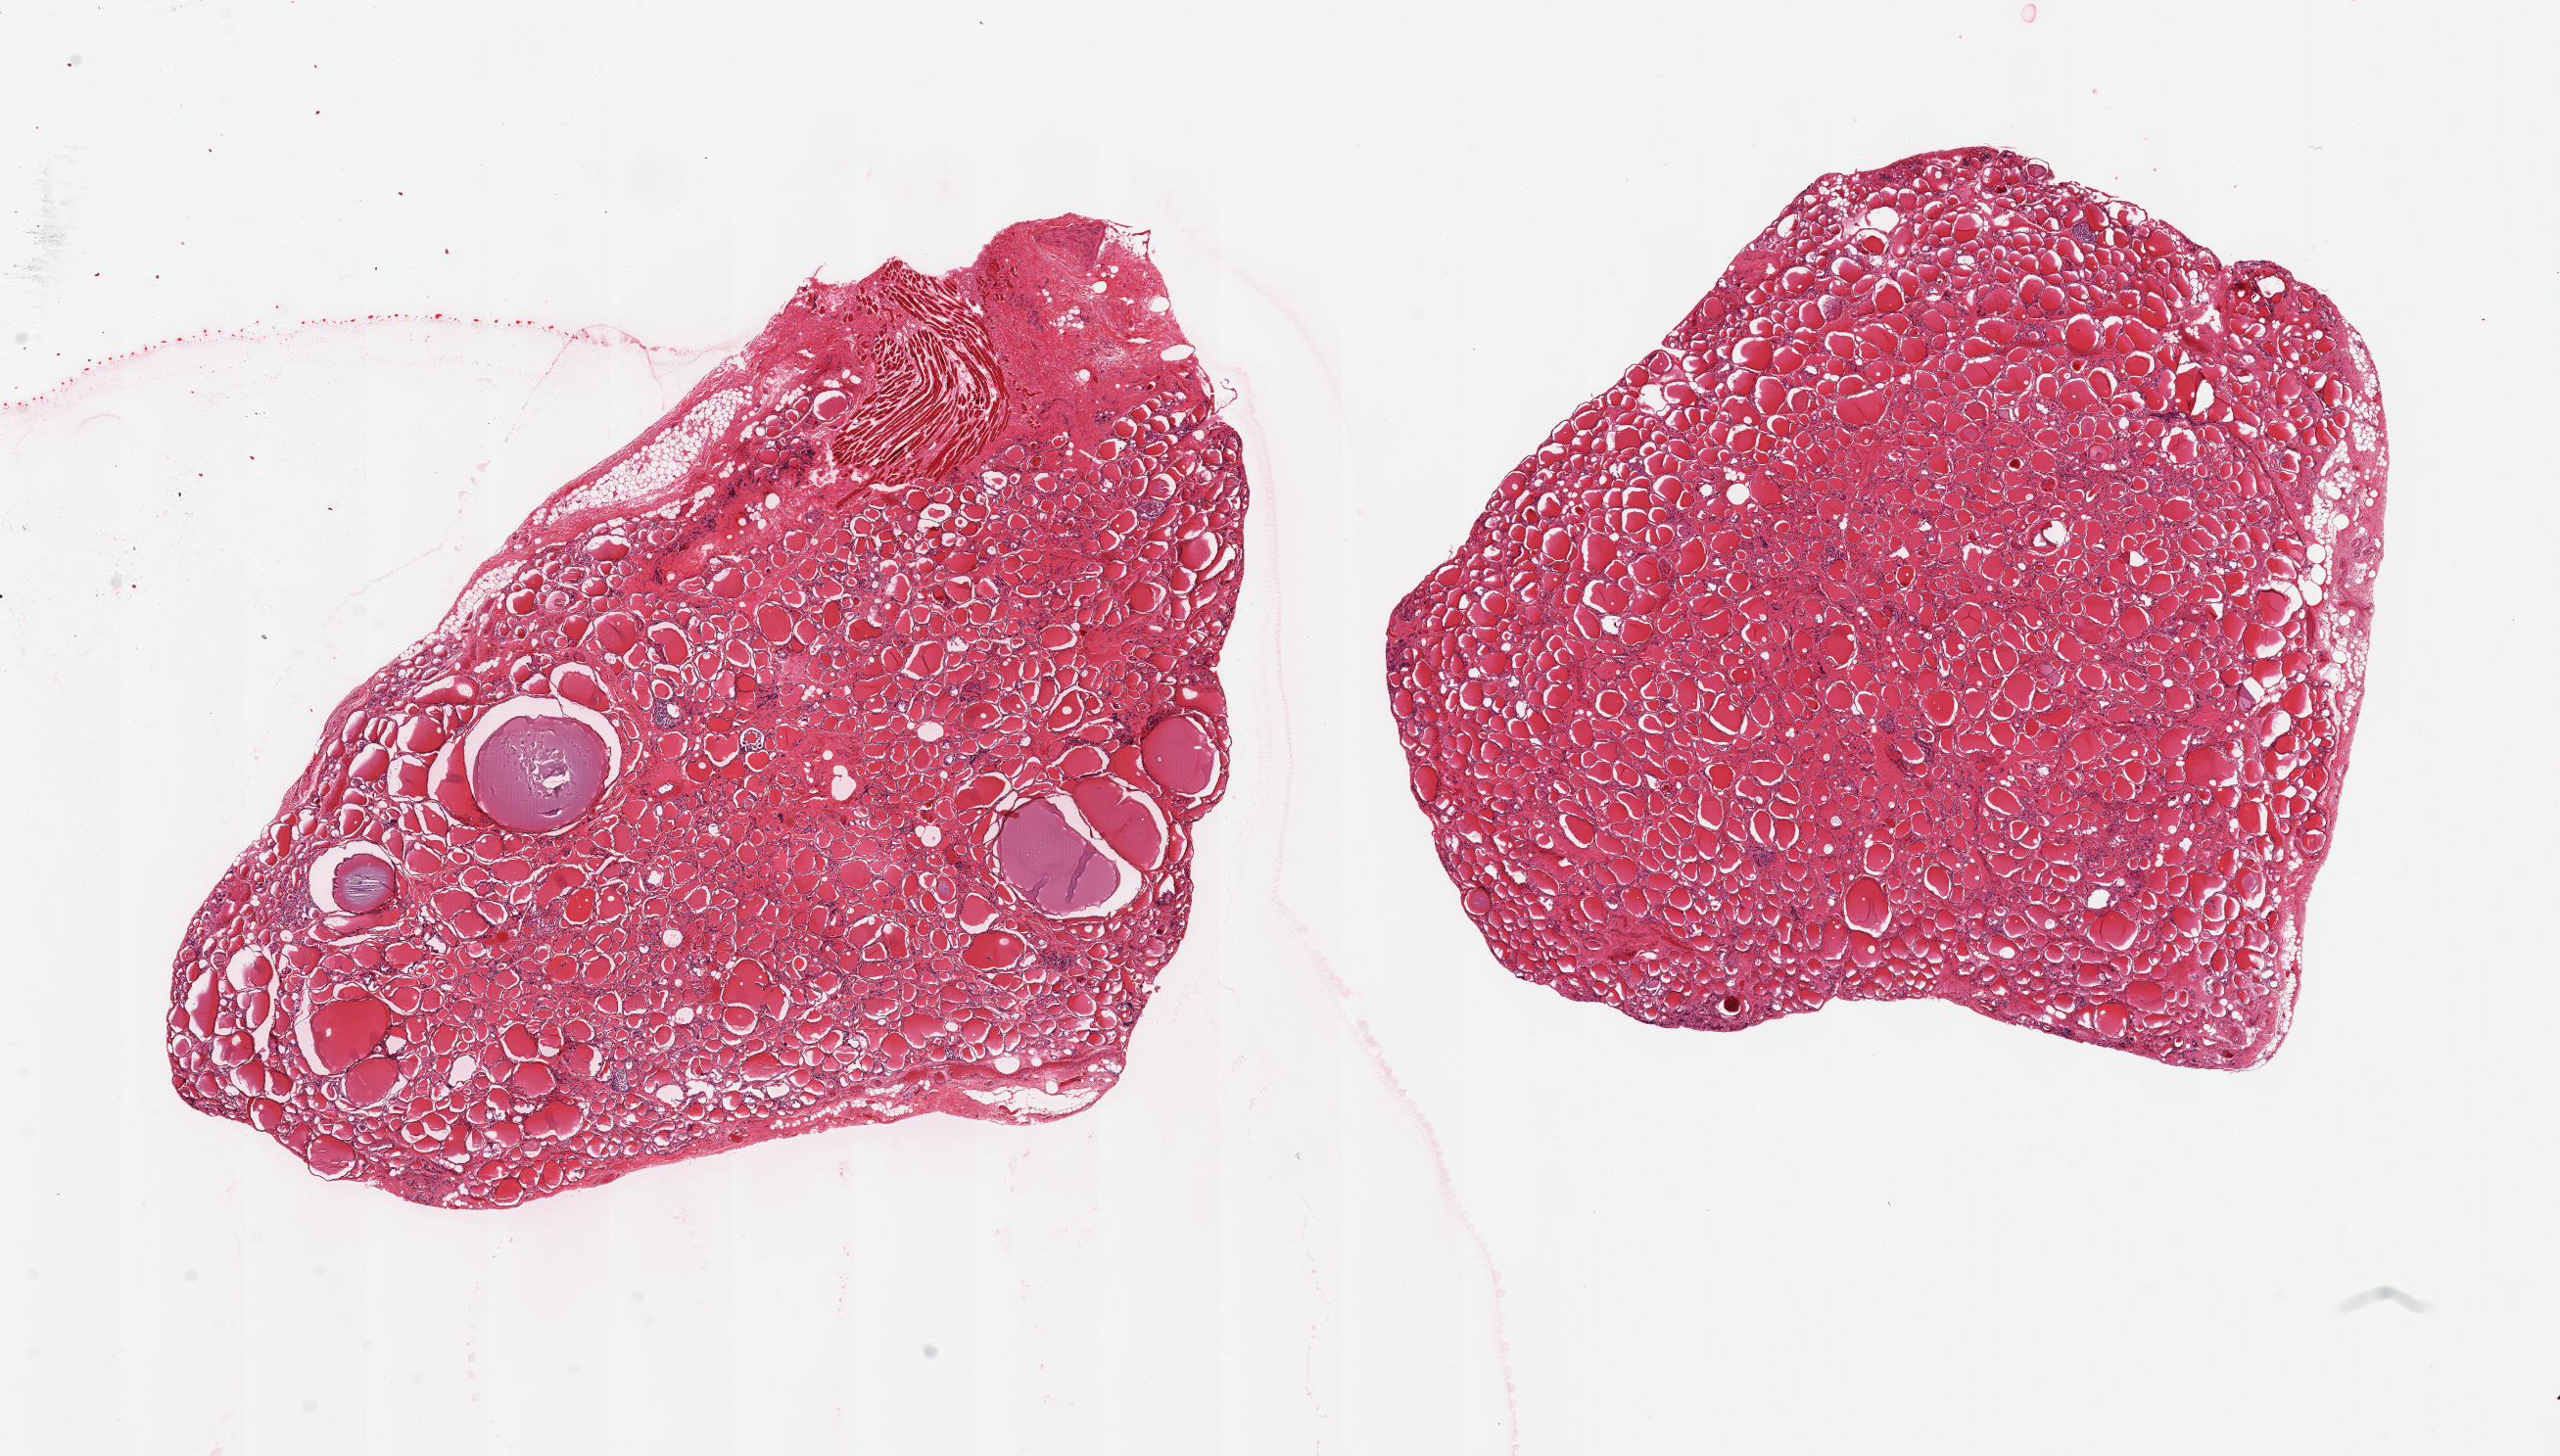
Digitized H&E-stained section, a low-resolution overview of the entire scanned area, about 20.7 x 11.8 mm, PAXgene-fixed, paraffin-embedded tissue, section of thyroid (target tissue), donor tissue sample.
- review note (as recorded): 2 pieces ~8x7mm; Multiple colloid cysts ~1mm